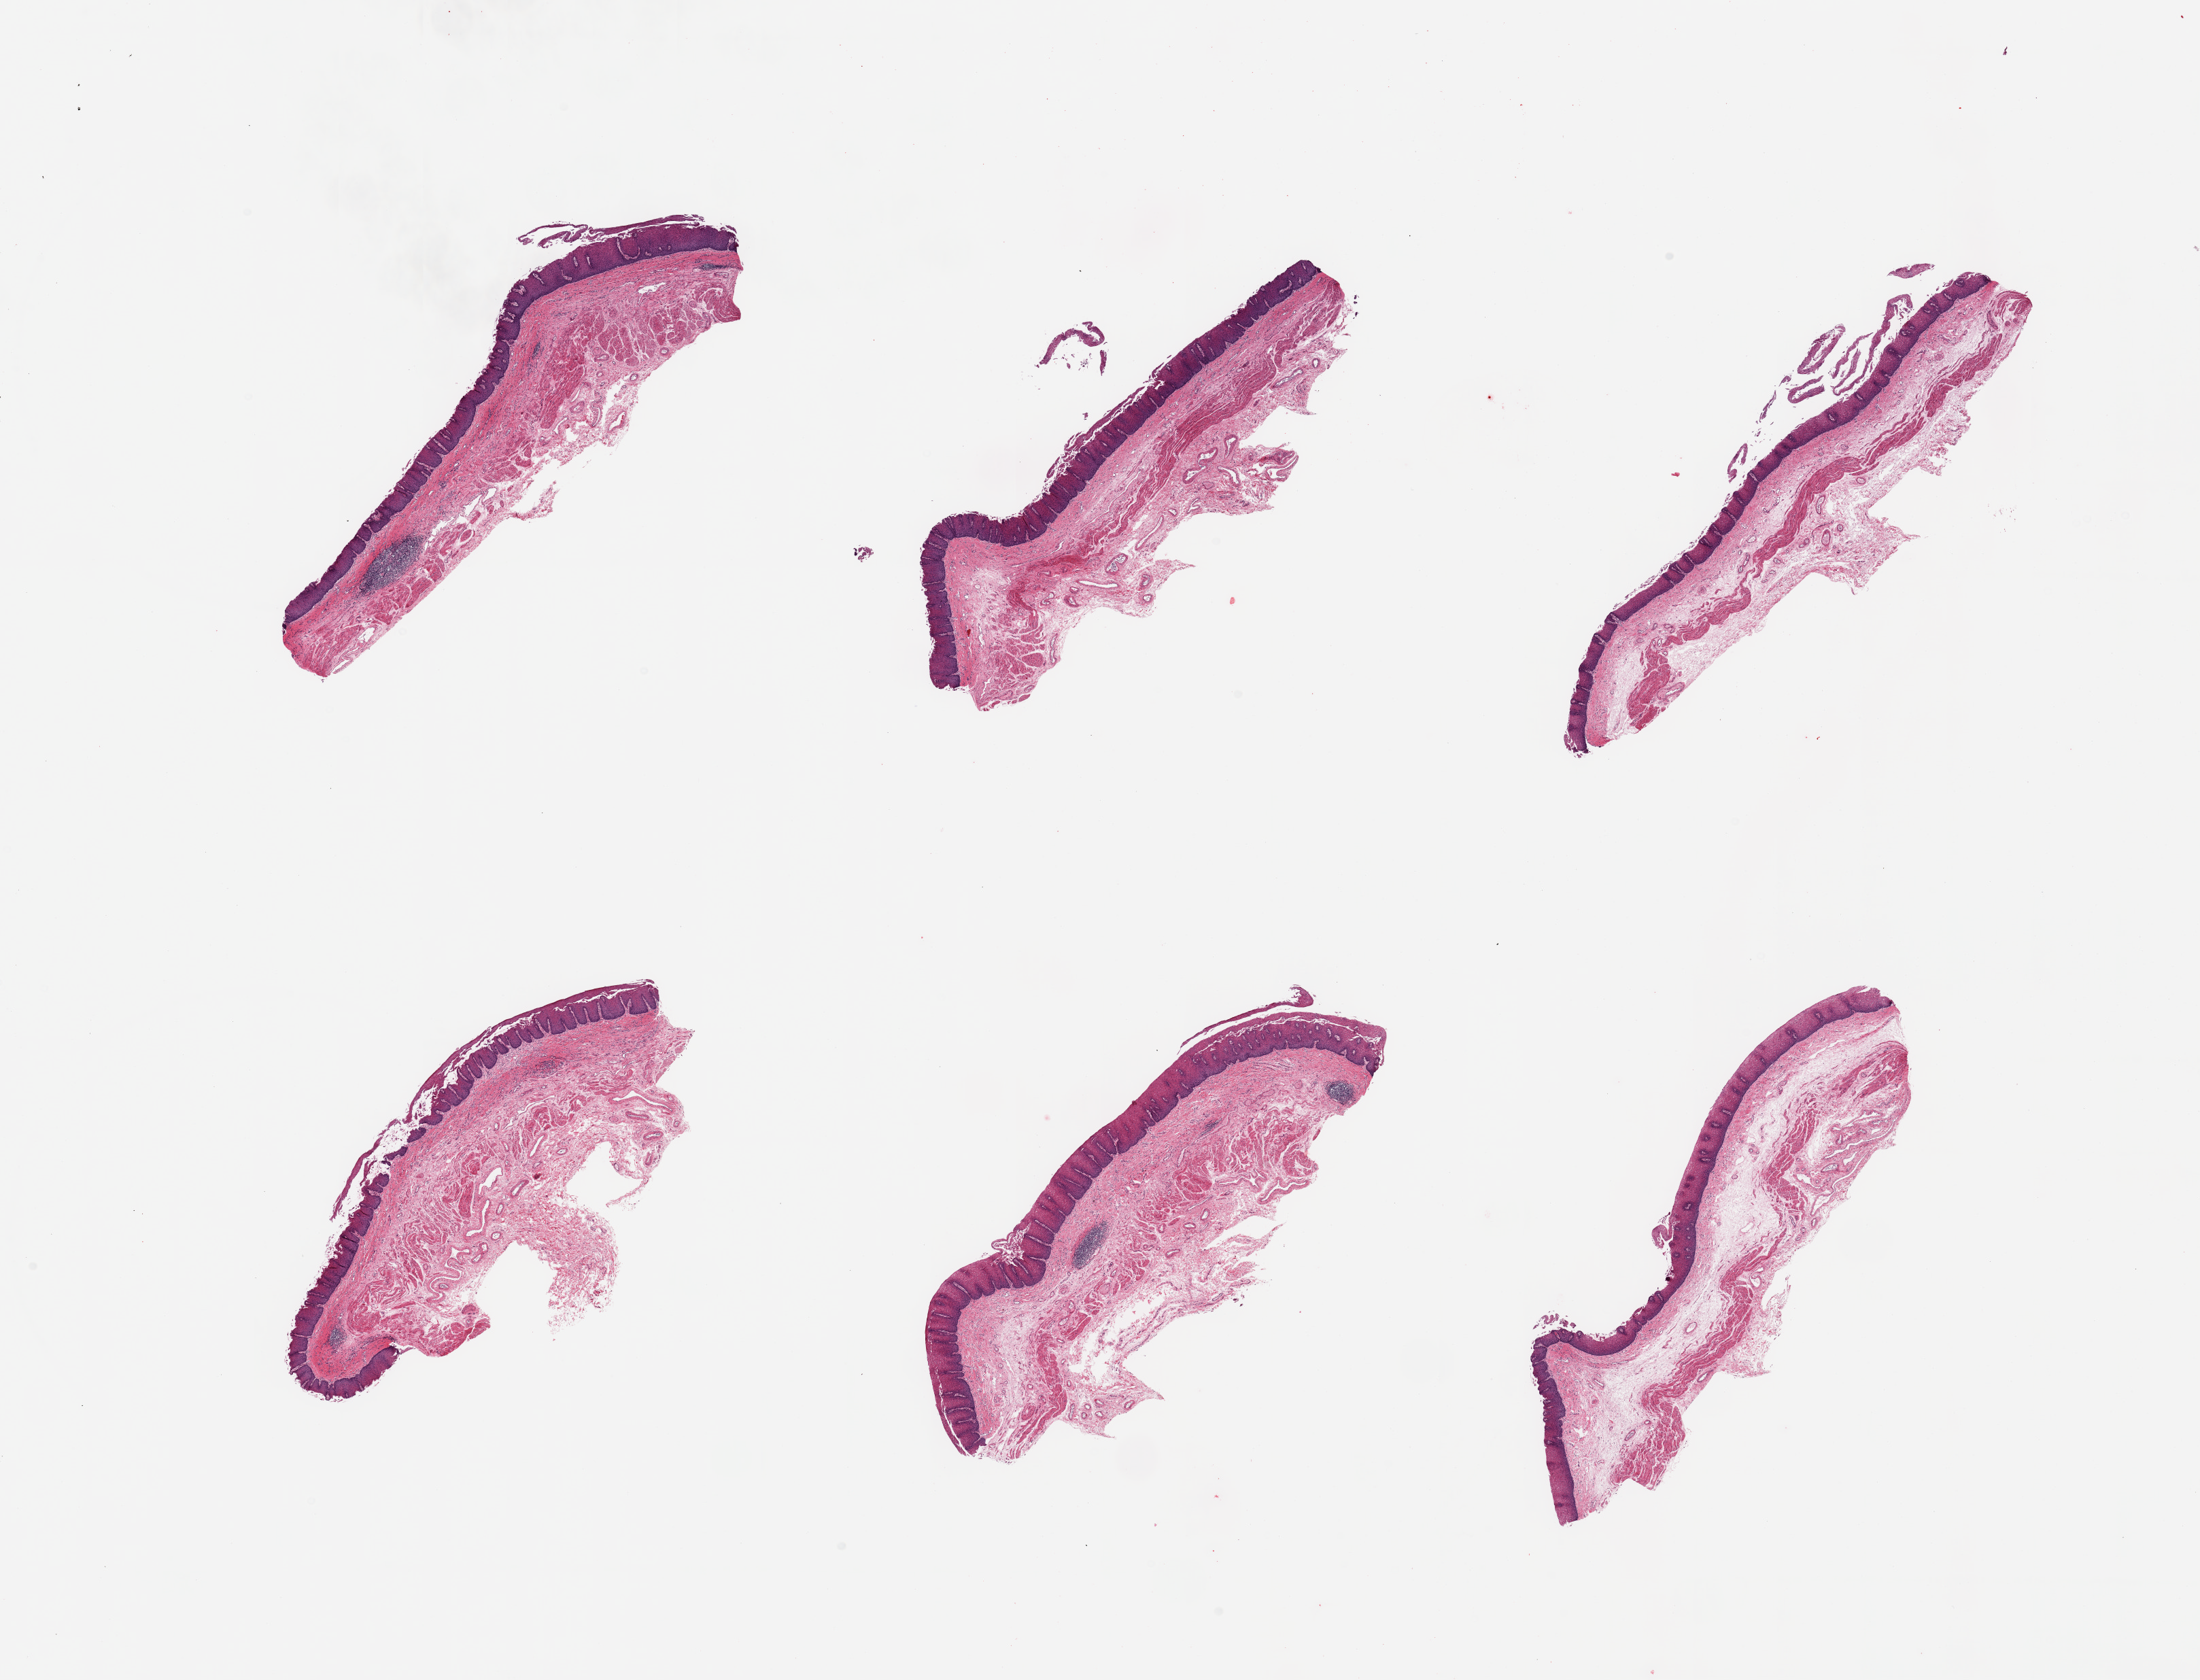
H&E whole-slide image — whole scanned area (about 25.6 x 19.5 mm) shown as a low-resolution overview, PAXgene-fixed, paraffin-embedded tissue, target tissue: esophageal mucous membrane, donor tissue sample. Female donor.
Review note (as recorded): 6 pieces; surface sloughing; reactive squamous thickening consistent with gastric reflux.